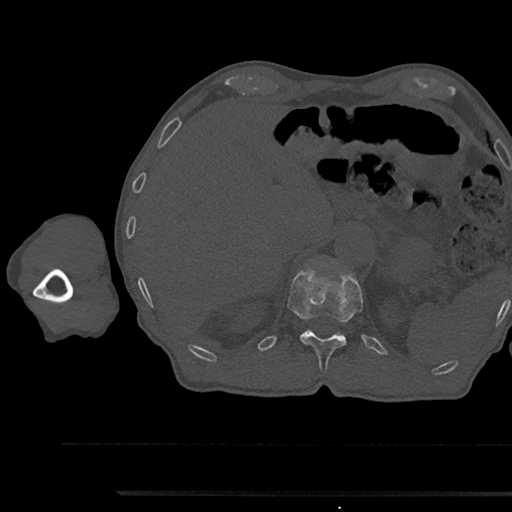
CT including the spine, one axial slice. Position 703 of 797 along the scan axis. Reconstruction kernel Br40s/3. Bone window (W 1800 / L 400 HU). 0.5 mm slice thickness. 512 × 512 image matrix, field of view 367 × 367 mm. Patient: male, 79 years. From the clinical record (not read from this slice): primary cancer: prostate.
Outlined on this slice (semi-automatically segmented with operator editing):
- T12 vertebra: bounding box (x1, y1, x2, y2) in pixels: (288, 271, 362, 372)